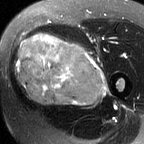
MRI of an extremity soft-tissue mass, one axial slice. Position 30 of 60 along the scan axis. T2-weighted fat-saturated. MR volume resampled by the dataset authors to the PET/CT grid (not the native acquisition matrix). 3.27 mm slice thickness. 144 × 144 image matrix, field of view 141 × 141 mm. Female patient. Case-level facts recorded for this patient, not image findings: histological type: pleiomorphic leiomyosarcoma; grade: intermediate; site of the primary tumour: left thigh.
Structures marked on this image (expert contour drawn on MRI and transferred to this co-registered scan by the dataset authors):
- gross tumour volume including surrounding oedema: bounding box [x1, y1, x2, y2] px = [15, 33, 108, 107]
- gross tumour volume (mass): [15, 35, 105, 105]